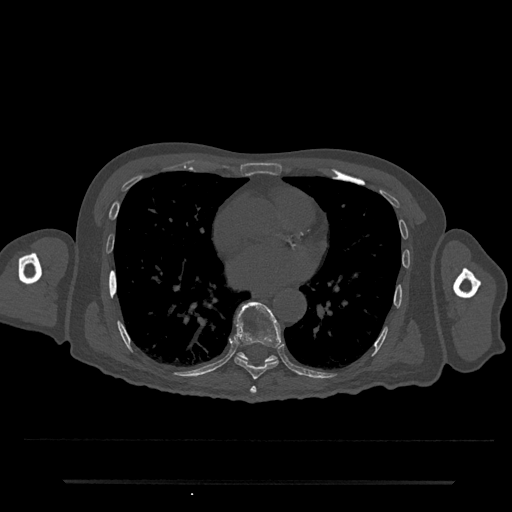
CT including the spine, one axial slice. Slice 408 of 797 in the series (ordered by position). 120 kVp. Bone window (W 1800 / L 400 HU). 512 × 512 image matrix, field of view 427 × 427 mm. Patient: male, 74 years. Case-level facts recorded for this patient, not image findings: primary cancer: prostate.
Outlined on this slice (semi-automatically segmented with operator editing):
- T7 vertebra: bounding box [x1, y1, x2, y2] px = [250, 386, 257, 394]
- T8 vertebra: [234, 301, 281, 380]
- T9 vertebra: [238, 352, 277, 362]